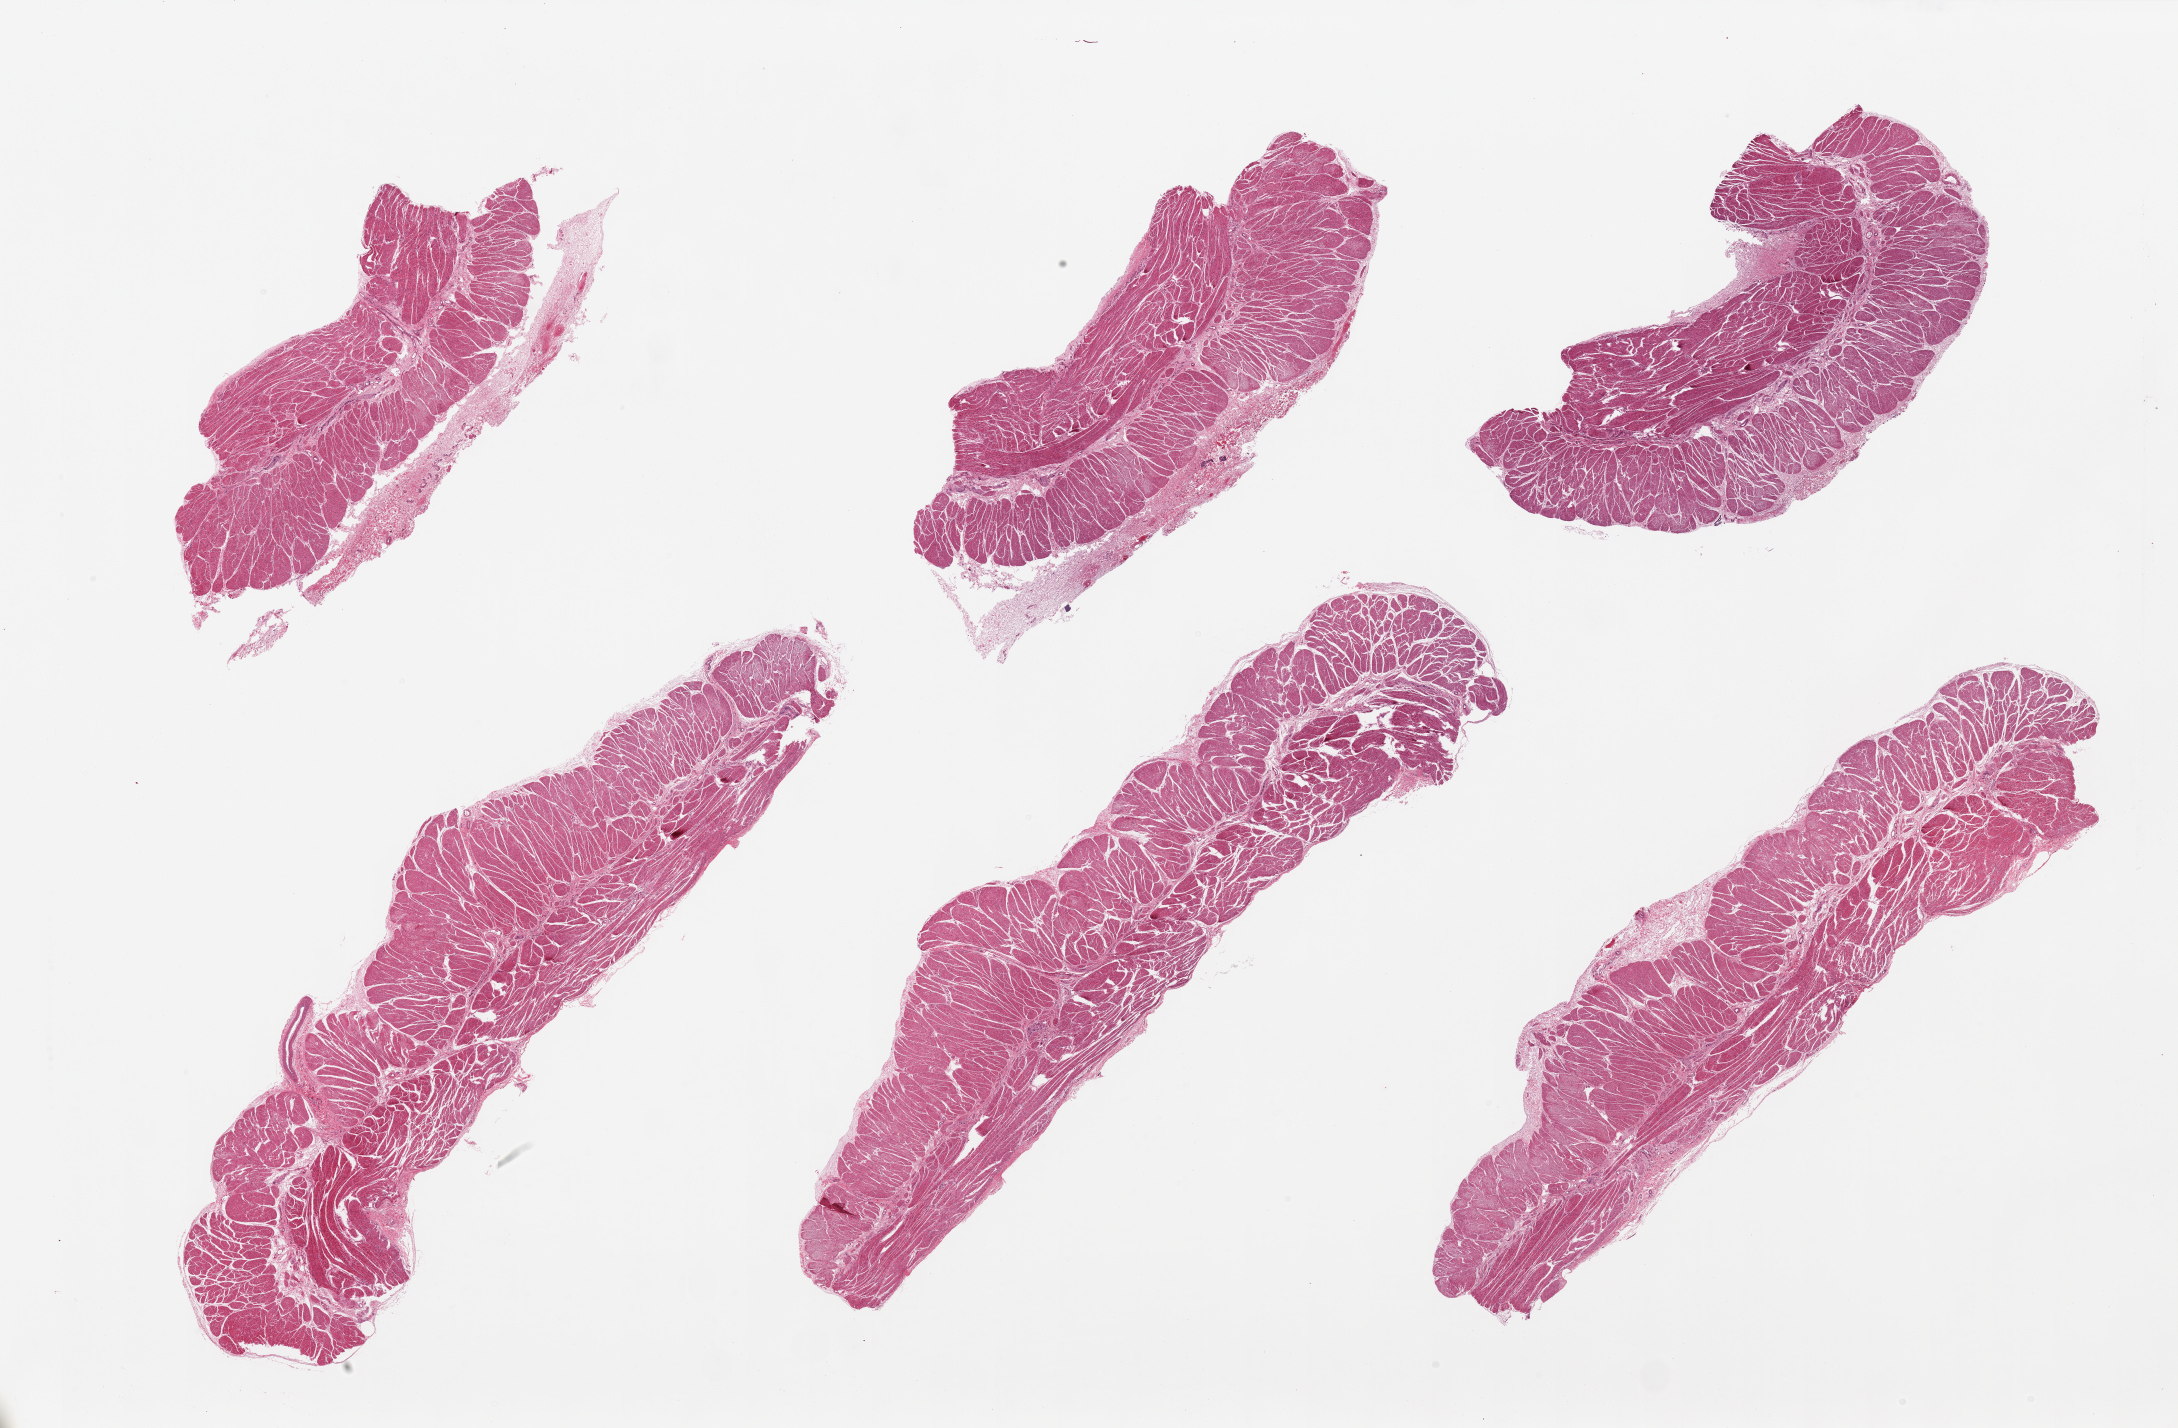
Digitized H&E-stained section — whole scanned area (about 34.5 x 22.6 mm, from a 20x scan) shown as a low-resolution overview. PAXgene-fixed paraffin-embedded (PFPE) section. Target tissue: esophageal muscle. Tissue donor sample. Female donor.
Reviewer comment on this tissue sample: 6 pieces, a few with up to 0.5mm strips of adherent serosa; All muscularis, good specimens.